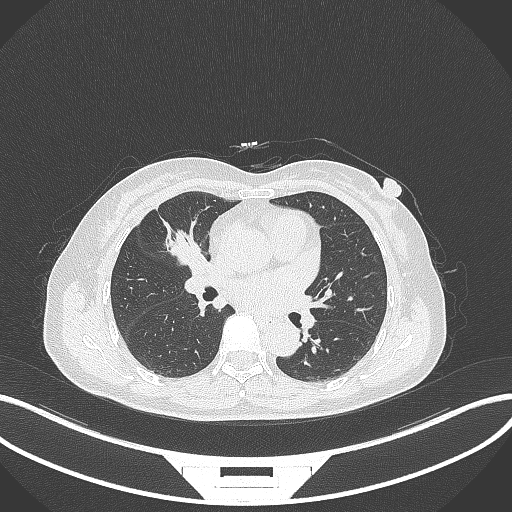
Chest CT, one axial slice; slice 158 of 284 in the series (ordered by position); reconstruction kernel B70f; 120 kVp; lung window (W 1500 / L -600 HU); 1 mm slice thickness; 512 × 512 image matrix, field of view 400 × 400 mm. Female patient, age 51 years. From the clinical record (not read from this slice): clinical TNM (as recorded): T1c N0 M0.
Outlined on this slice (rectangle marked by the reading radiologist):
- lung tumour (recorded histology: adenocarcinoma): box from (x=161, y=225) to (x=204, y=269) px